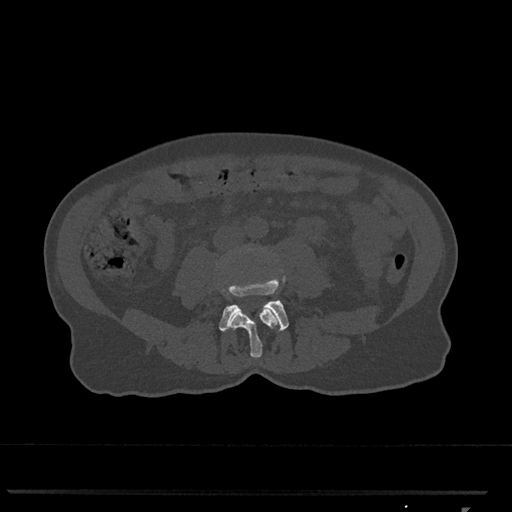
CT including the spine, one axial slice. Position 238 of 793 along the scan axis. Reconstruction kernel Br40s/3. 120 kVp. Bone window (W 1800 / L 400 HU). 0.5 mm slice thickness. 512 × 512 image matrix, field of view 380 × 380 mm. Female patient, age 62 years. From the clinical record (not read from this slice): primary cancer: renal.
Outlined on this slice (semi-automatic segmentation, software-assisted and operator-edited):
- L3 vertebra: bounding box <230,250,280,358> (left, top, right, bottom; pixels)
- L4 vertebra: <219,277,289,331>